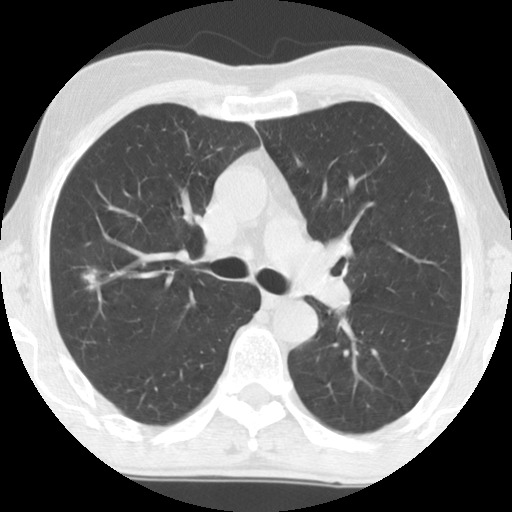
Low-dose screening chest CT, axial slice; first (baseline) screen; lung window (W 1500 / L -600 HU); standard (soft-tissue) reconstruction kernel (STANDARD); slice 47 of 133 in the series; 512 × 512 image matrix, field of view 310 × 310 mm. Male participant, aged 69 years at enrolment. Former smoker at enrolment.
Expert reader's lesion annotation, box from (x=56, y=251) to (x=122, y=314) px. The exam's reader record, not a measurement of the box and not confirmed to be the same lesion: non-calcified nodule or mass ≥4 mm, right upper lobe, 8 × 8 mm, spiculated (stellate) margins, soft tissue attenuation. Official screen result: positive, change unspecified: nodule(s) >= 4 mm or enlarging nodule(s), mass(es), or other non-specific abnormalities suspicious for lung cancer. Later outcome: lung cancer diagnosed 588 days after this screen (after the second annual screen) — mucinous adenocarcinoma, right upper lobe, moderately differentiated (G2), stage IA (AJCC 6th edition), 11 mm at pathology.